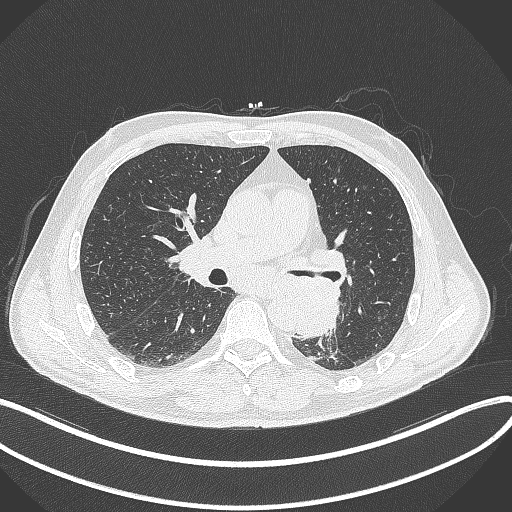
Chest CT, one axial slice; position 191 of 329 along the scan axis; reconstruction kernel B70f; 120 kVp; lung window (W 1500 / L -600 HU); 1 mm slice thickness; 512 × 512 image matrix, field of view 400 × 400 mm. Patient: male, 59 years. Case-level facts recorded for this patient, not image findings: clinical TNM (as recorded): T2a N2 M0.
Structures marked on this image (bounding box drawn by a radiologist):
- lung tumour (recorded histology: squamous cell carcinoma): bounding box (x1, y1, x2, y2) in pixels: (291, 275, 341, 341)